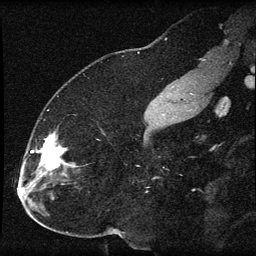
Breast MRI (dynamic contrast-enhanced), one sagittal slice. Position 28 of 60 along the scan axis. Dynamic contrast-enhanced series, image 2 of 3 at this slice position (ordered by acquisition). 1.5 T. TE 4.2 ms, TR 8.2 ms. 256 × 256 image matrix, field of view 180 × 180 mm. Patient: female, 32 years.
Structures marked on this image (semi-automatic segmentation, software-assisted and operator-edited):
- analysis volume of interest (the breast-tissue region the enhancement analysis was run in; not a lesion): bounding box <31,132,75,184> (left, top, right, bottom; pixels)
- tumour enhancement mask (voxels above the 70 % enhancement threshold inside the analysis volume of interest): <31,135,65,174>